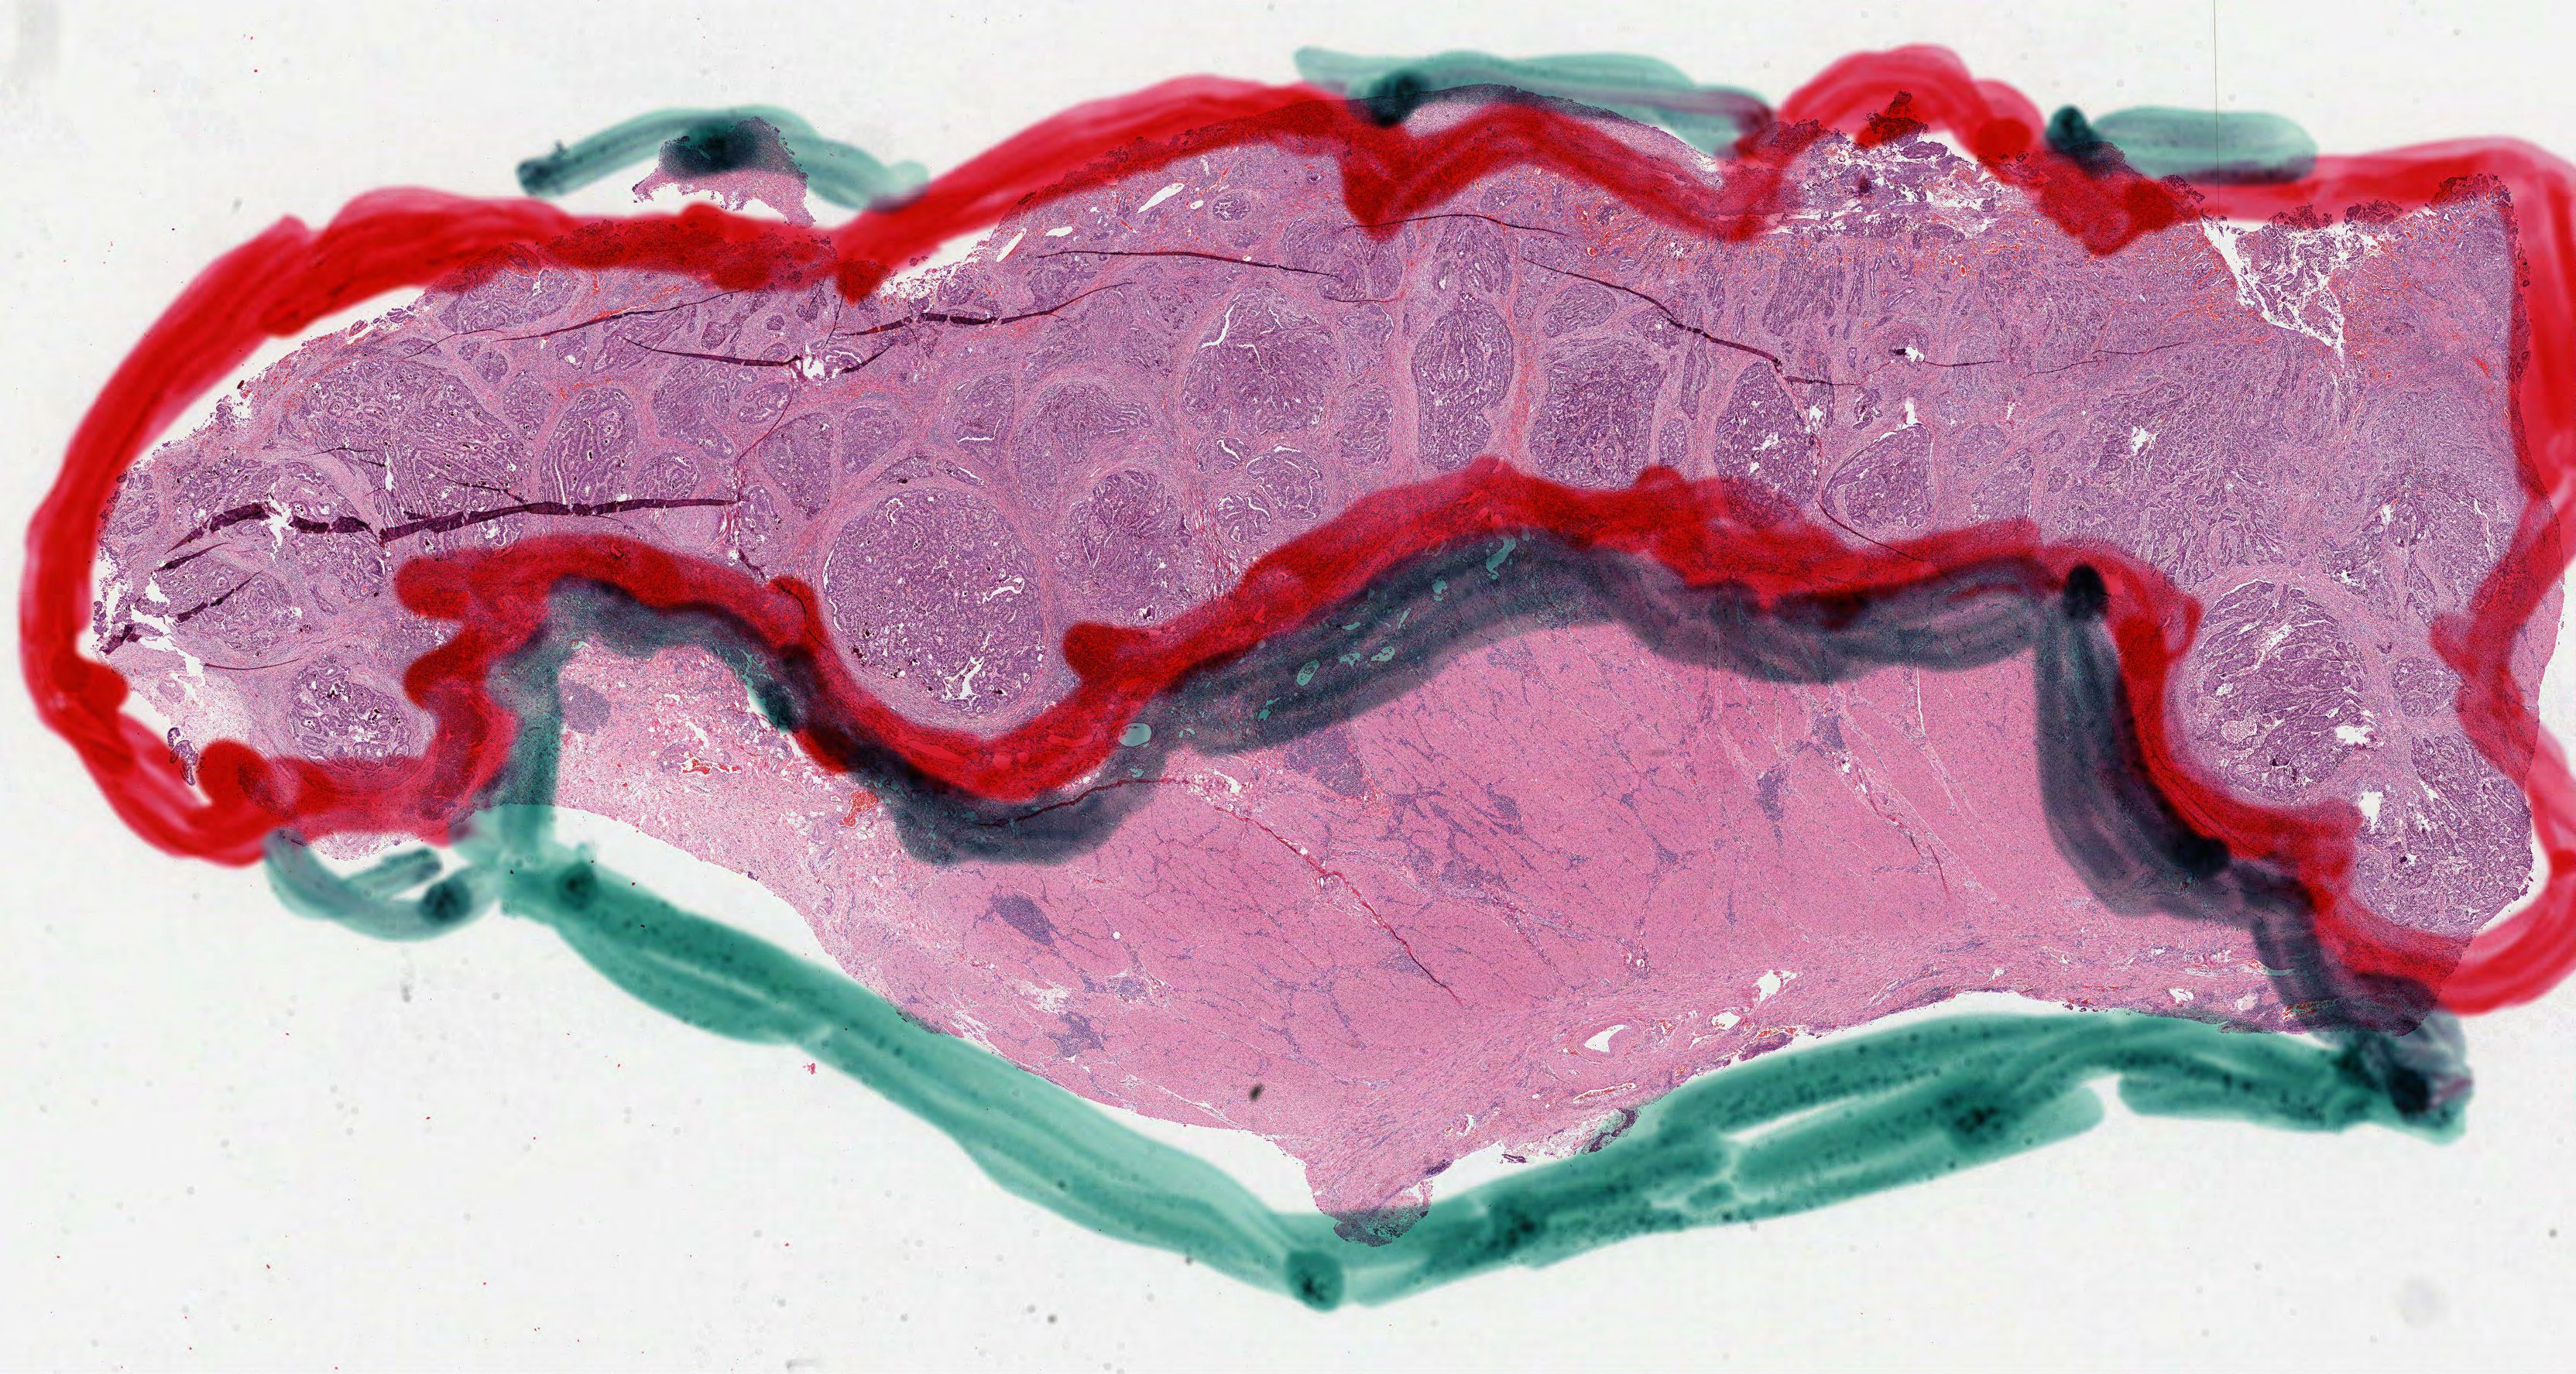
Hematoxylin and eosin (H&E) stained whole-slide image — whole scanned area (about 26.8 x 14.3 mm) shown as a low-resolution overview; formalin-fixed paraffin-embedded (FFPE) diagnostic section; stomach, primary tumour sample. Female, age 58 years at initial diagnosis.
Diagnosis: Adenocarcinoma, intestinal type (body of stomach).